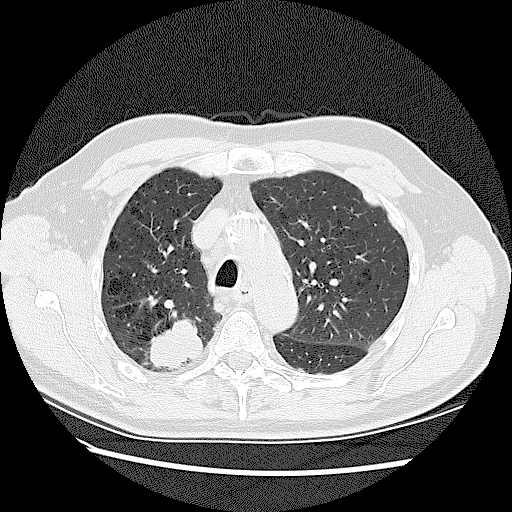
Low-dose screening chest CT, one axial slice; reconstruction kernel LUNG; 120 kVp; lung window (W 1500 / L -600 HU); 512 × 512 image matrix.
Structures marked on this image (expert manual segmentation):
- lesion 2 (tumor, upper lobe of right lung): bounding box (x1, y1, x2, y2) in pixels: (150, 320, 204, 369)